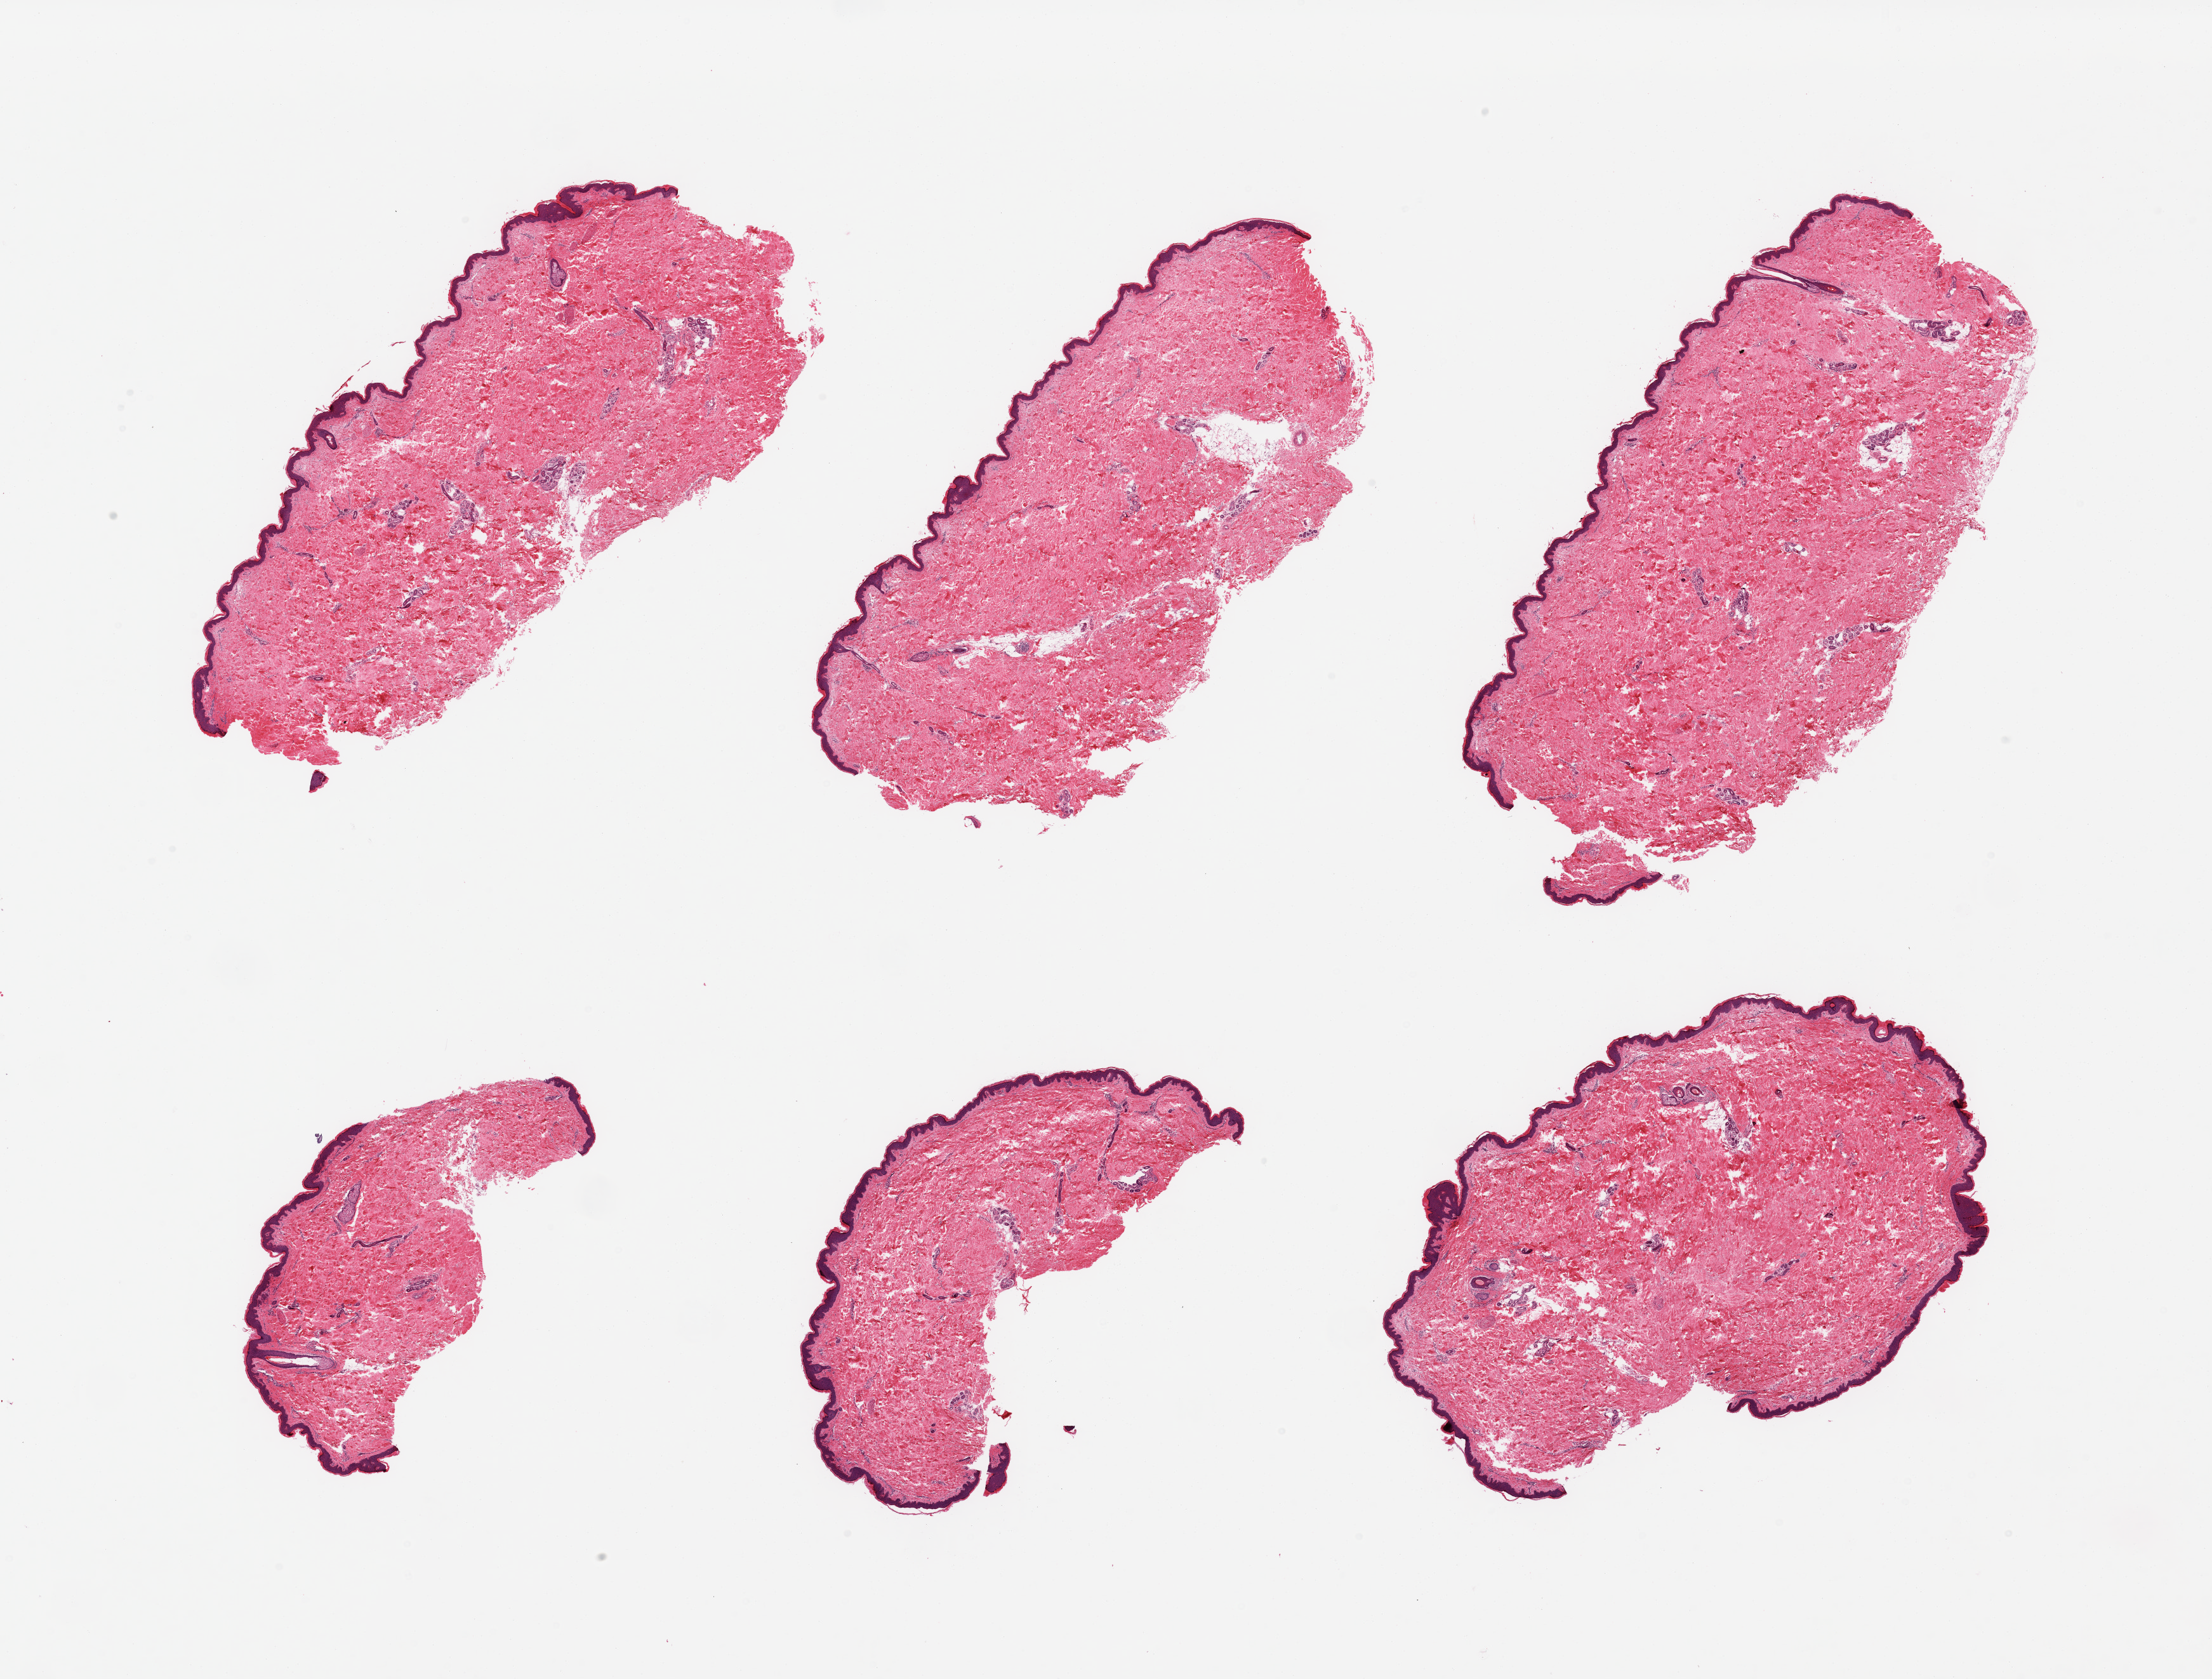
Haematoxylin and eosin whole-slide image — shown as a low-resolution overview of the whole scanned area (about 27.6 x 20.9 mm); PAXgene-fixed paraffin-embedded (PFPE) section; section of skin of lower leg (target tissue); donor tissue sample. Male donor.
Pathologist's review note for this sample: 6 pieces, no significant dermal fat; squamous epithelium is ~50-60 microns.